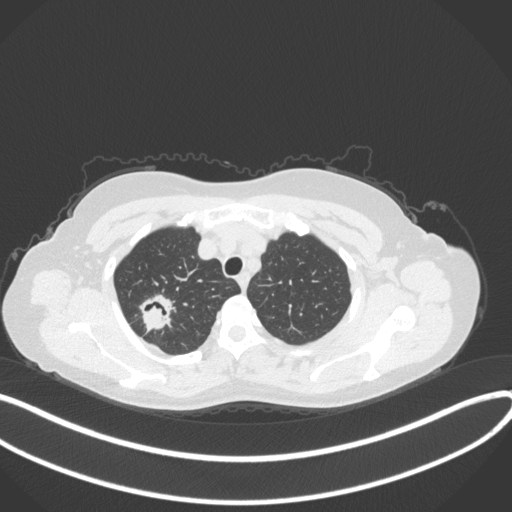
Chest CT, one axial slice; position 302 of 342 along the scan axis; 120 kVp; lung window (W 1500 / L -600 HU); 1 mm slice thickness; 512 × 512 image matrix. Female patient, age 50 years. From the clinical record (not read from this slice): clinical TNM (as recorded): T1c N0 M0; histopathological grade: G2-3.
Structures marked on this image (bounding box drawn by a radiologist):
- lung tumour (recorded histology: adenocarcinoma): bounding box <136,293,175,333> (left, top, right, bottom; pixels)